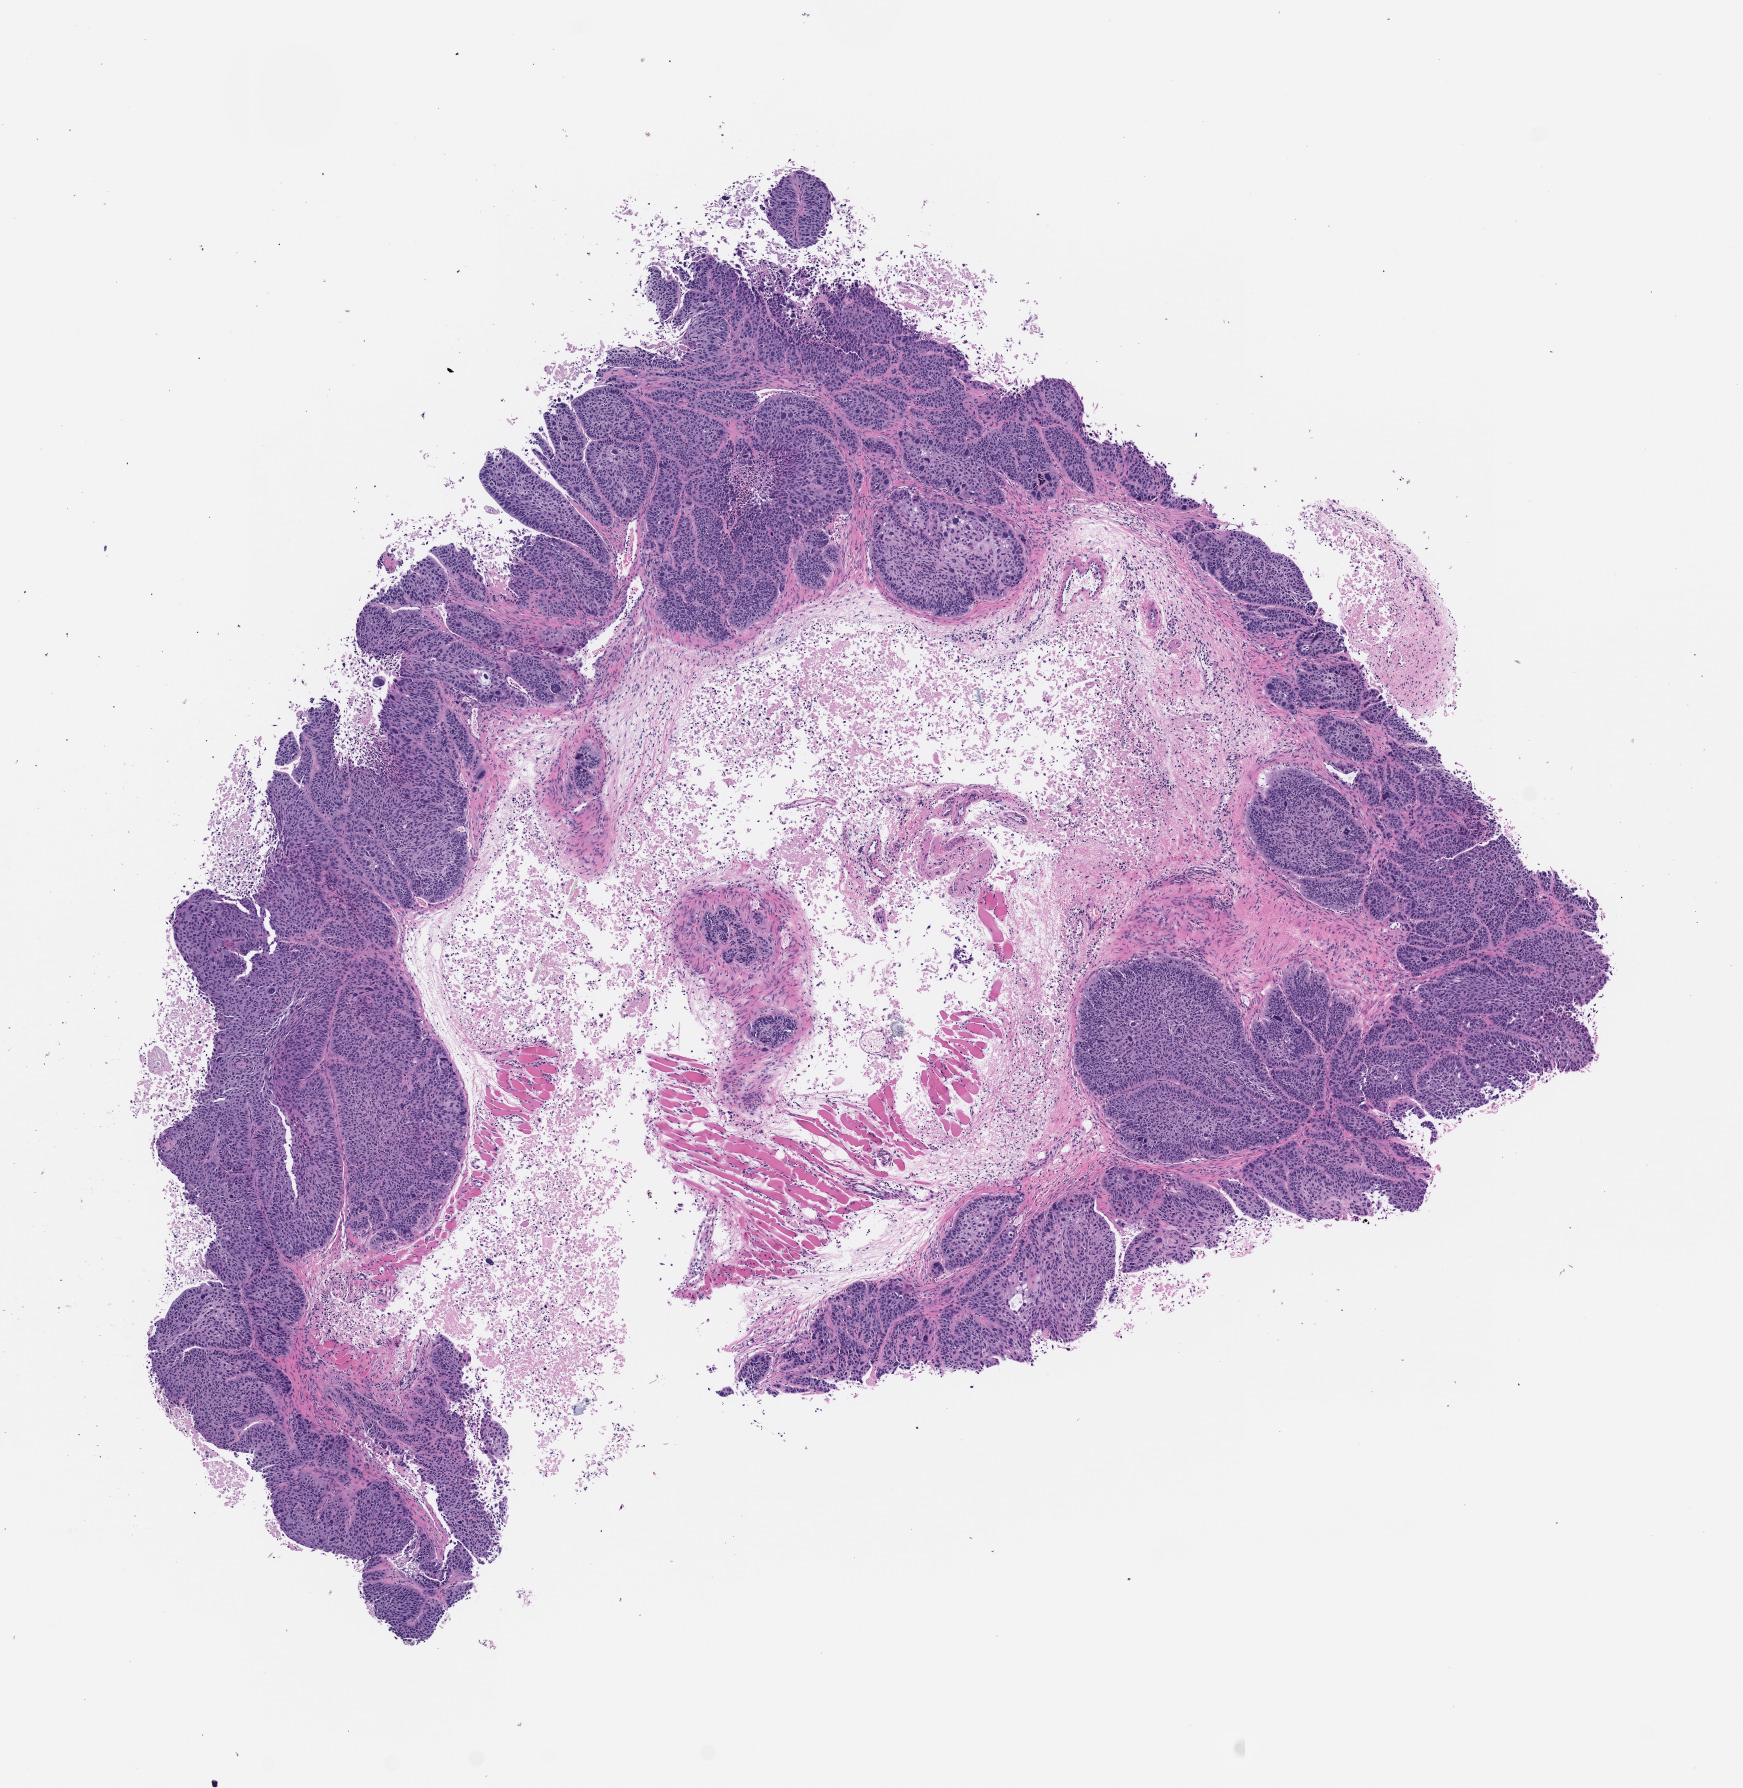
Whole-slide image, H&E: patient-derived xenograft (human tumor grown in a mouse) — shown as a low-resolution overview of the whole scanned area (about 7.0 x 7.2 mm), formalin-fixed paraffin-embedded section, originating tumor site category: lung.
Originating patient diagnosis: Lung Squamous Cell Carcinoma.